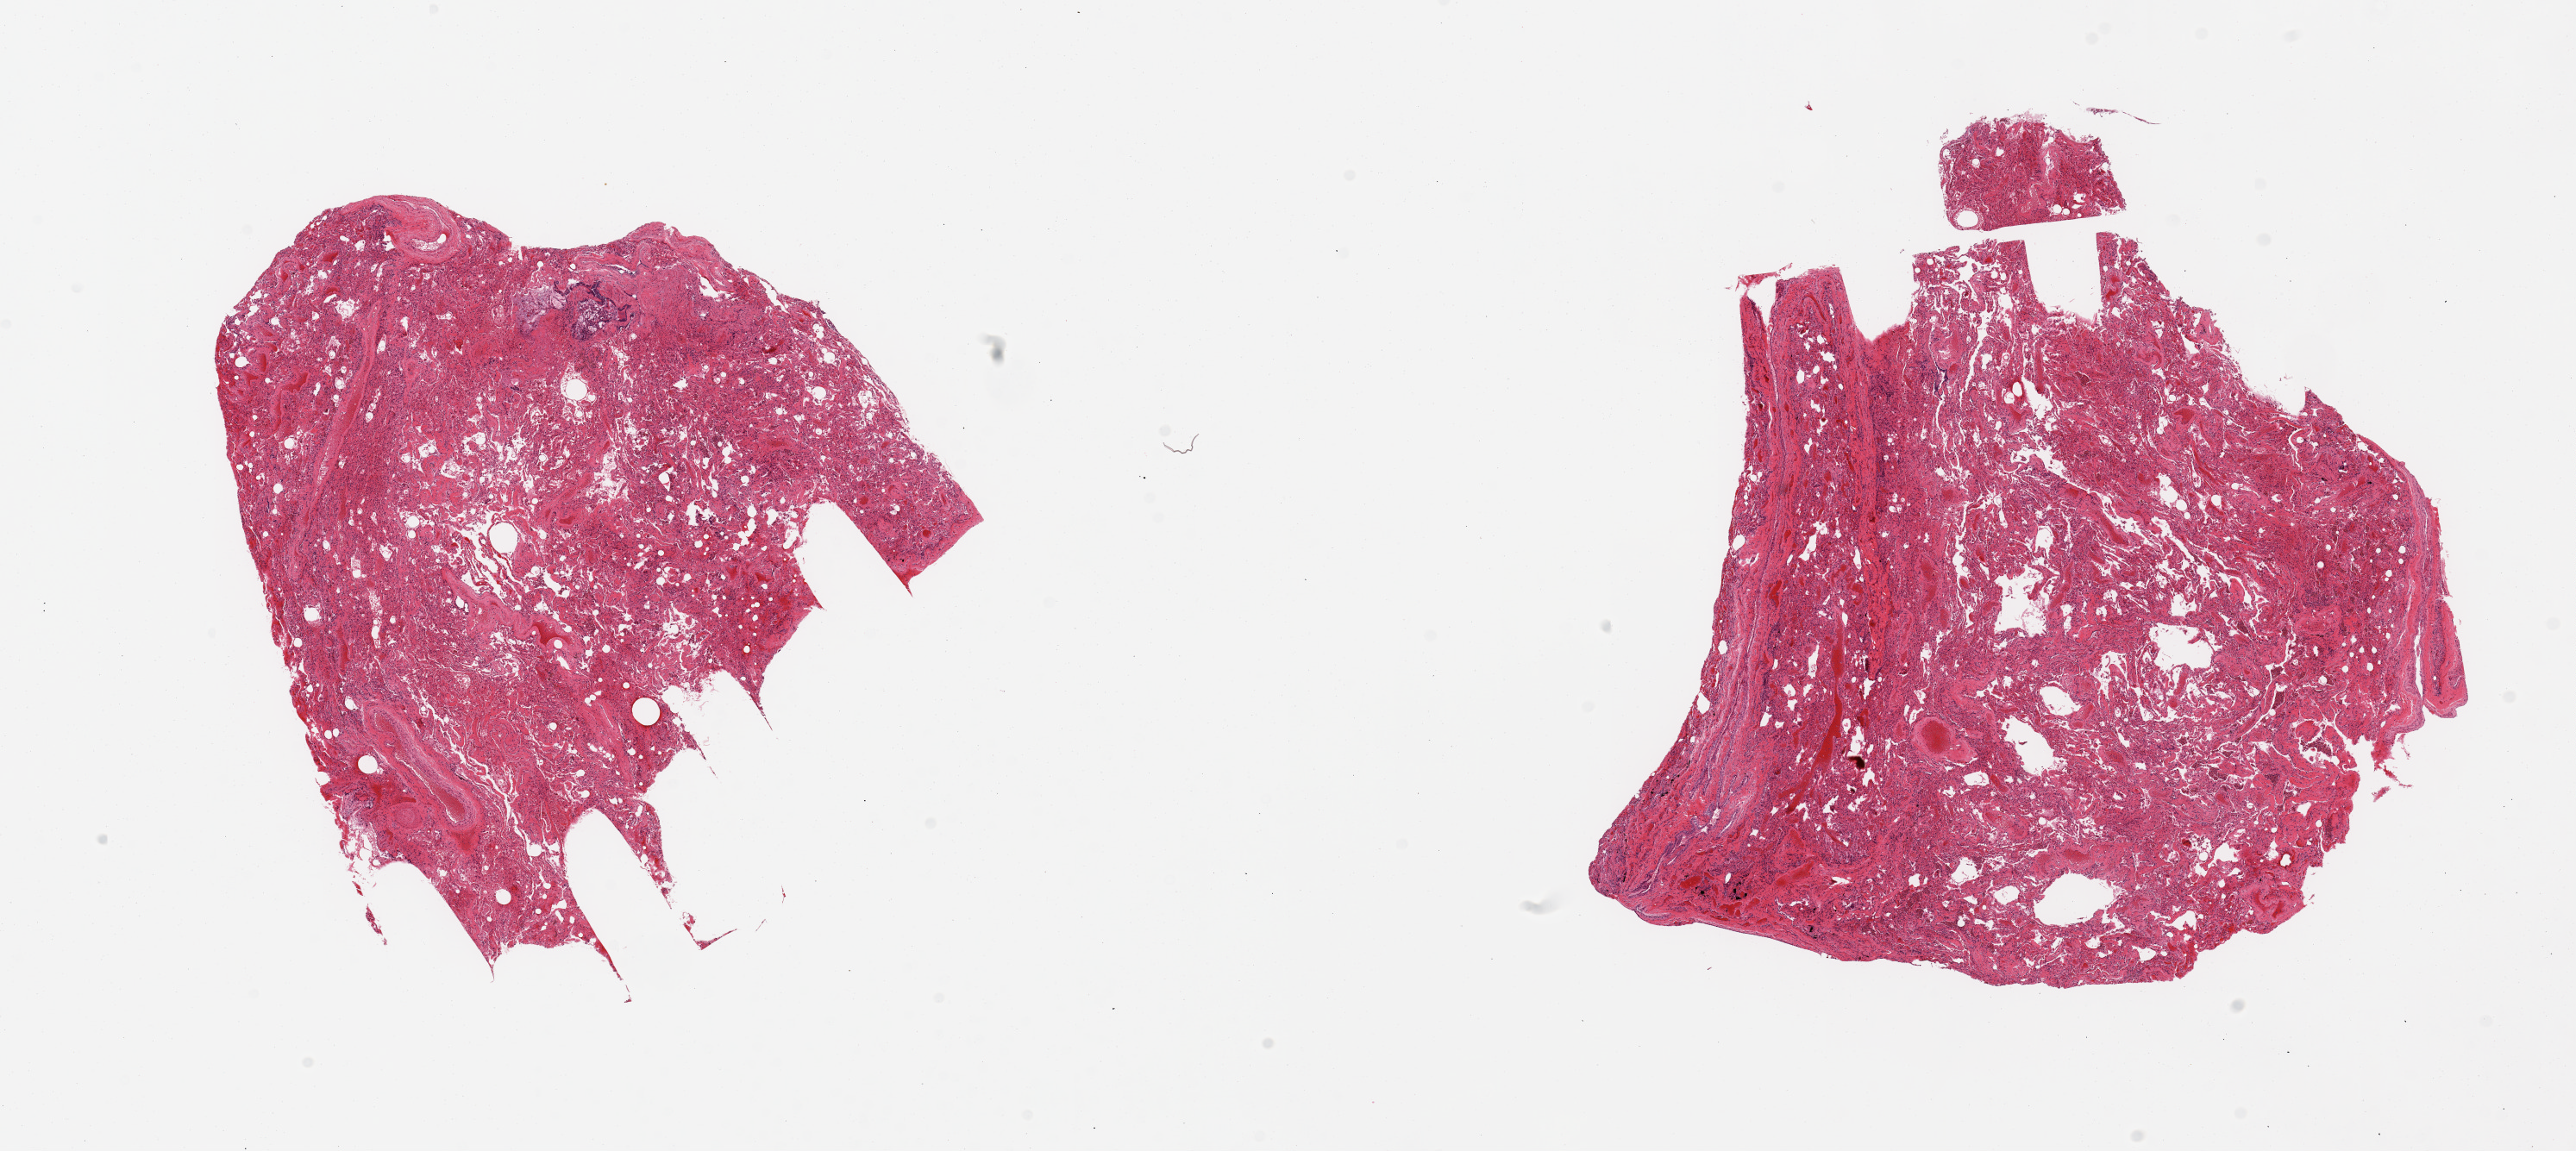
Digitized H&E-stained section — whole scanned area (about 23.6 x 10.6 mm, slide scanned at 20x) shown as a low-resolution overview. PAXgene-fixed, paraffin-embedded tissue. Sampled site (target tissue): lung. Donor tissue sample. Male donor.
Review note (as recorded): 2 pieces, moderate congestion.